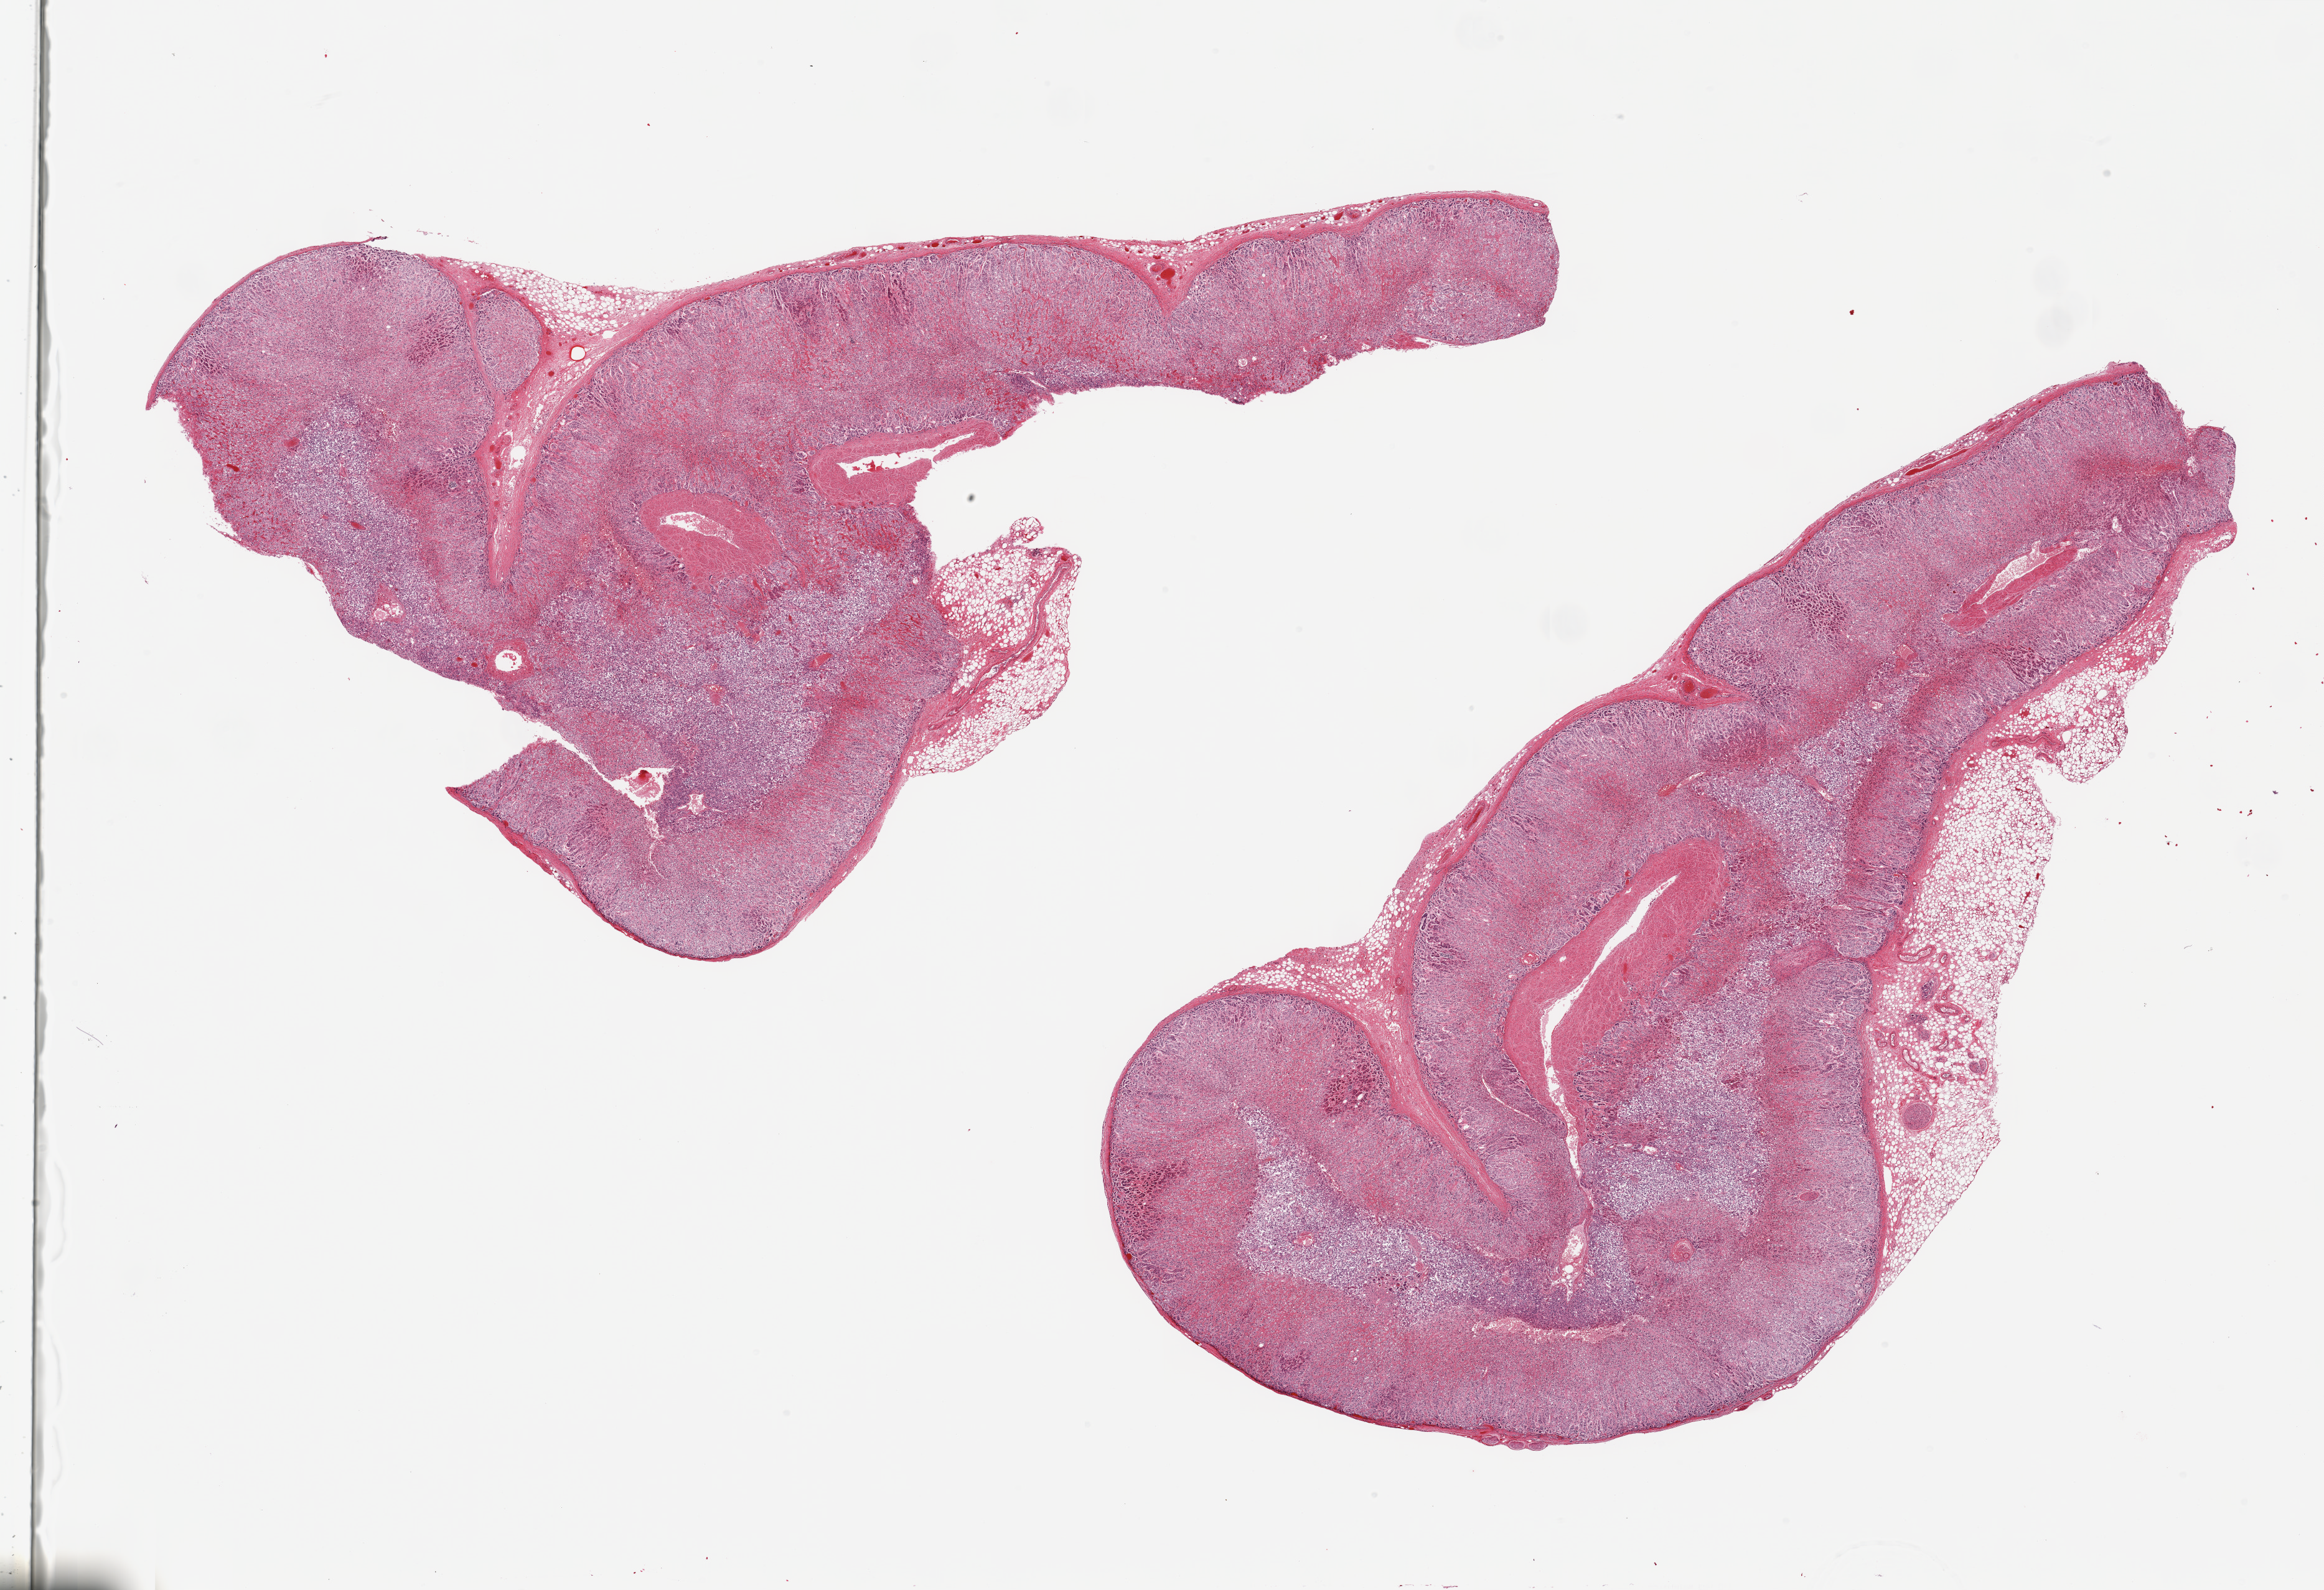
Digitized hematoxylin and eosin (H&E)-stained section — a low-resolution overview of the entire scanned area, about 29.5 x 20.2 mm; PAXgene-fixed, paraffin-embedded tissue; sampled site (target tissue): adrenal gland; donor tissue sample. Male donor.
Review note (as recorded): 2 pieces, ~20% medulla and cortex; Nubbin of adherent fat, 8x1.3mm.